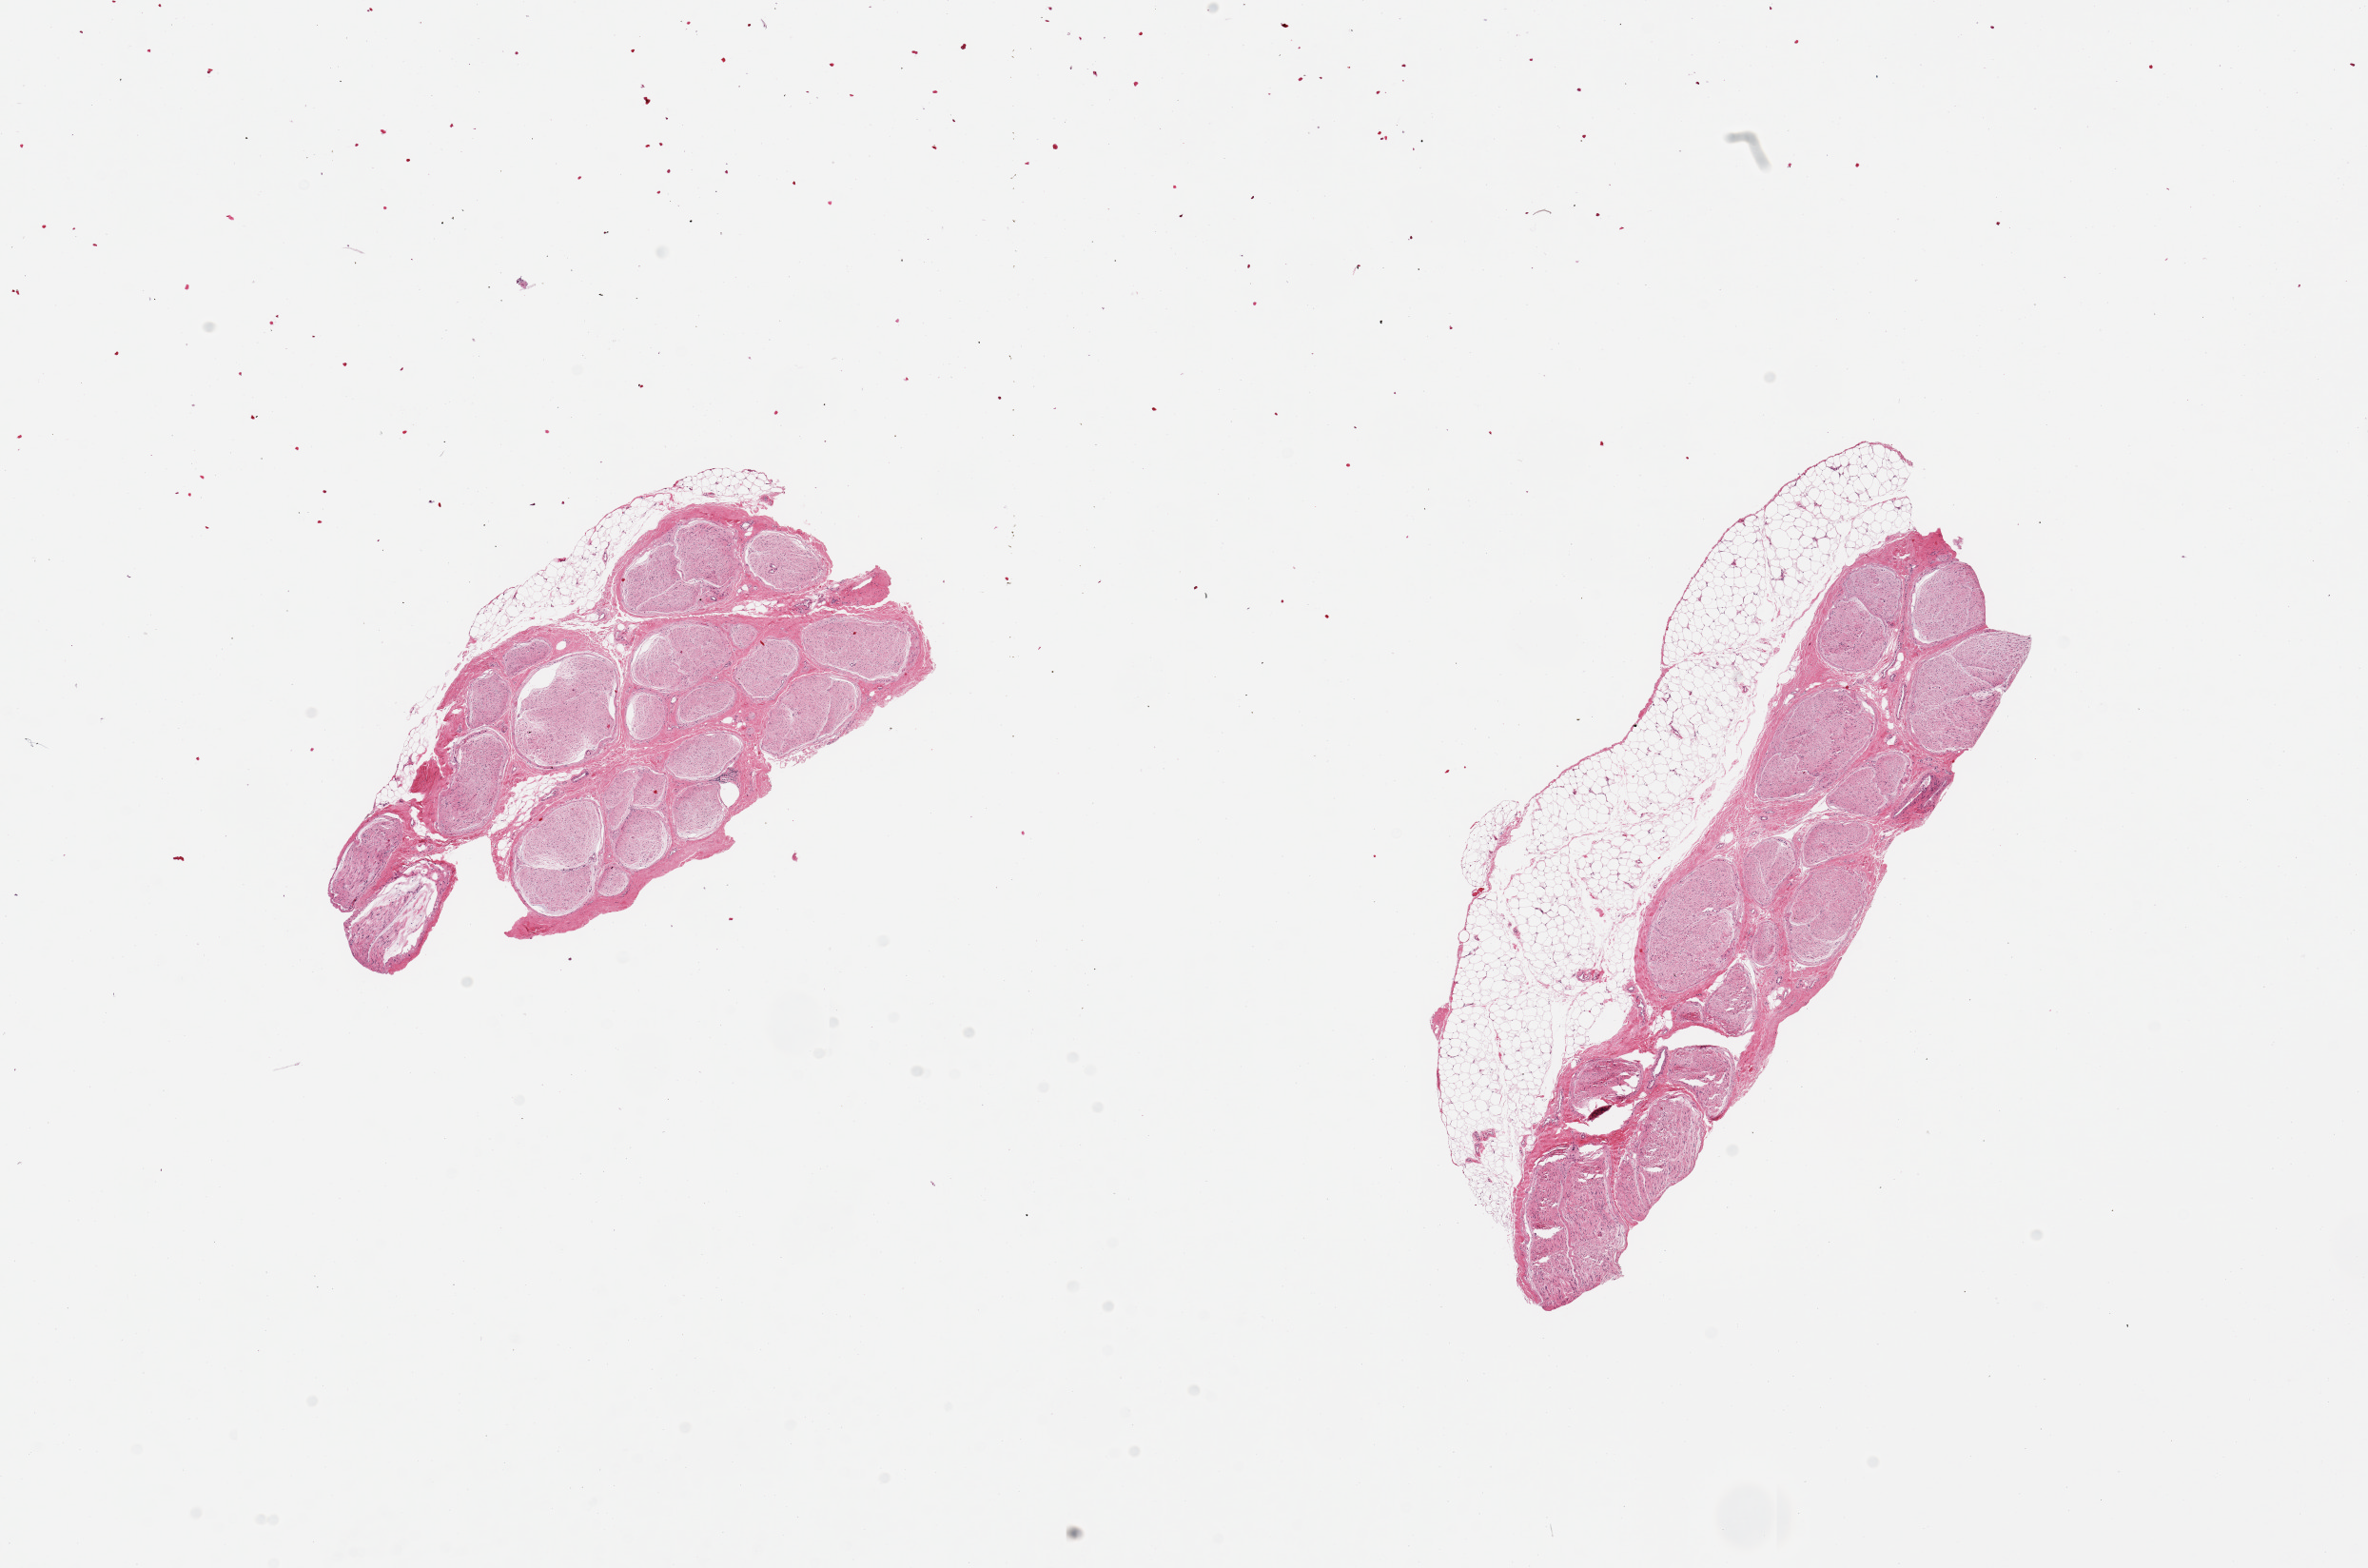
Whole-slide image, H&E stain — whole scanned area (about 19.7 x 13.0 mm) shown as a low-resolution overview, PAXgene-fixed paraffin-embedded (PFPE) section, target tissue: tibial nerve, tissue donor sample. Donor: female.
Pathologist's review note for this sample: 2 pieces, rim of fat up to ~1mm.